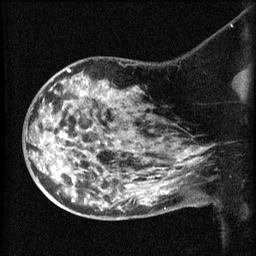
Breast MRI (dynamic contrast-enhanced), one sagittal slice; dynamic contrast-enhanced series, image 2 of 3 at this slice position (ordered by acquisition); 1.5 T; TE 4.2 ms, TR 8.2 ms; 256 × 256 image matrix. Female patient, age 50 years.
Annotated regions visible in this slice (semi-automatic segmentation, software-assisted and operator-edited):
- analysis volume of interest (the breast-tissue region the enhancement analysis was run in; not a lesion): bounding box (x1, y1, x2, y2) in pixels: (38, 75, 169, 211)
- tumour enhancement mask (voxels above the 70 % enhancement threshold inside the analysis volume of interest): (83, 91, 85, 94)